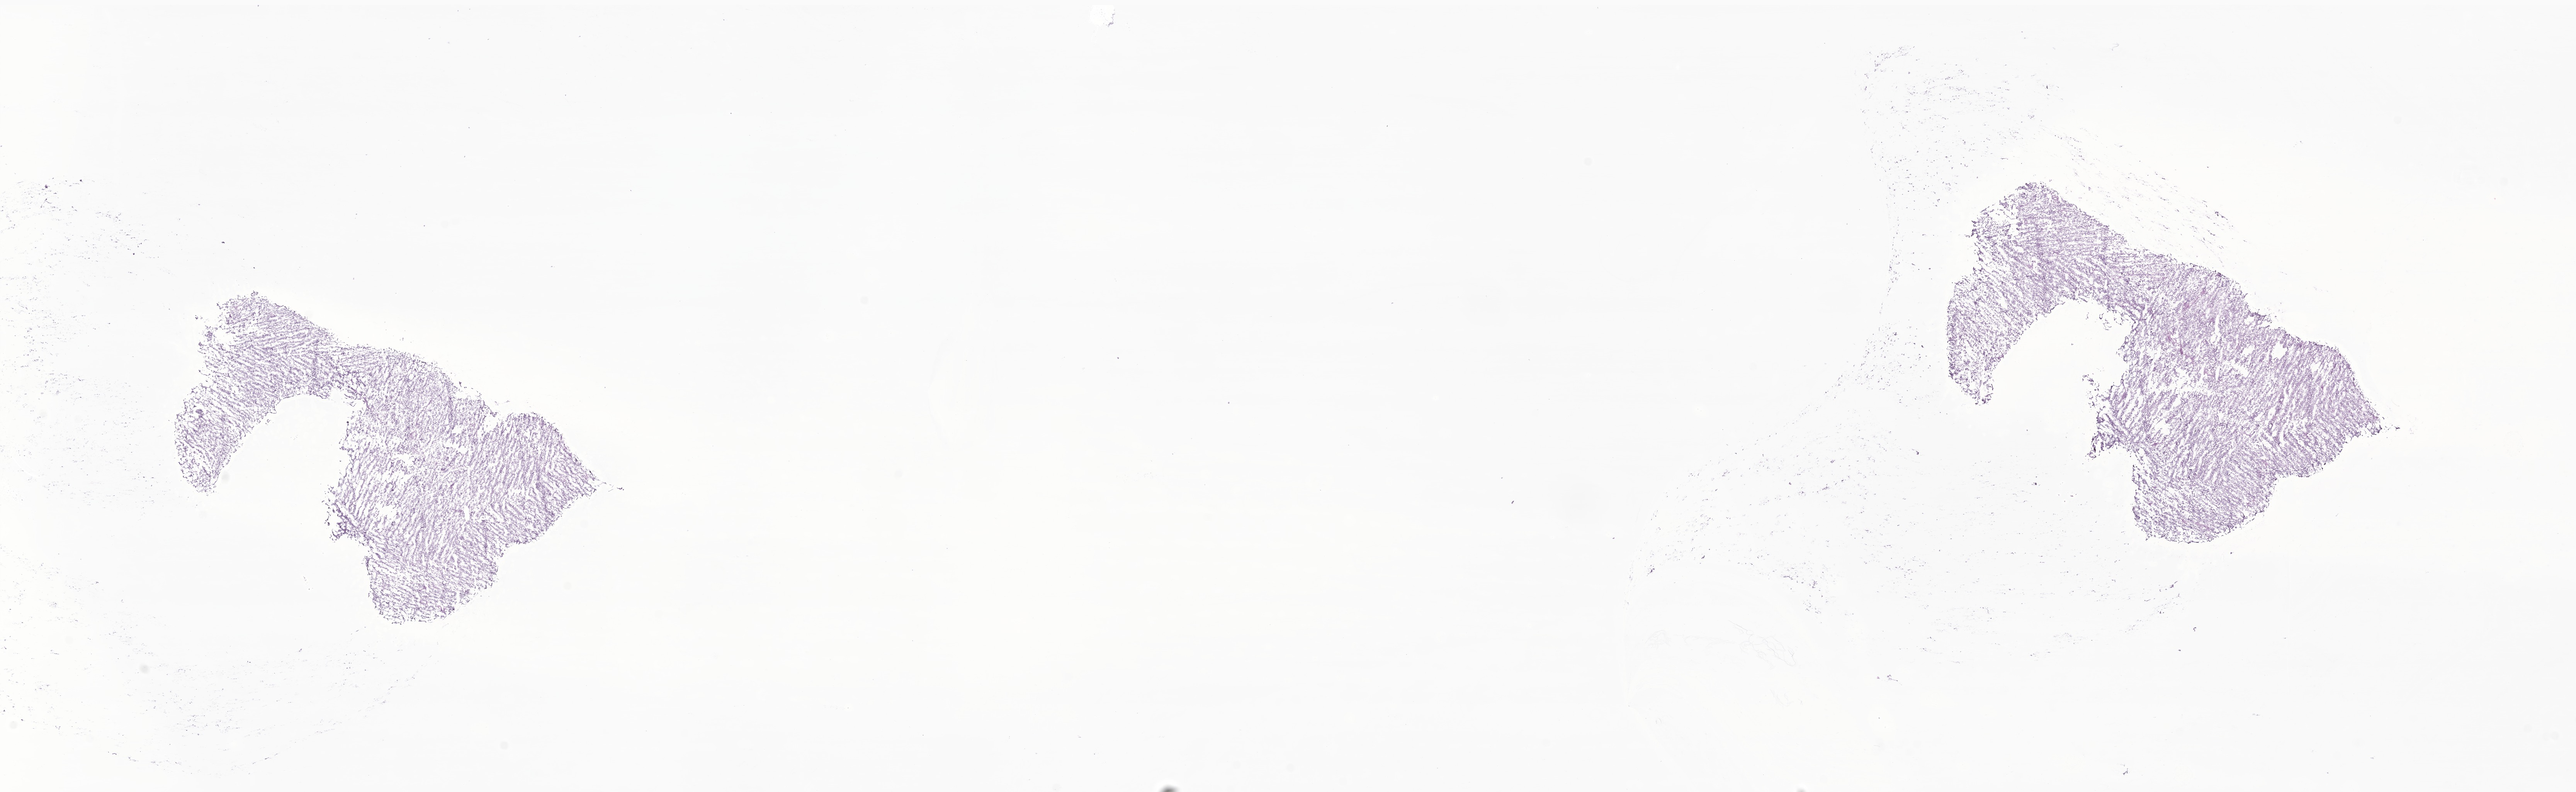
Digitized haematoxylin and eosin-stained section of tumor tissue from the brain — whole scanned area (about 28.1 x 8.6 mm) shown as a low-resolution overview, frozen section. Patient: female, age 91 months (7 years 7 months).
Diagnosis (ICD-O-3 morphology term): Neoplasm, malignant.